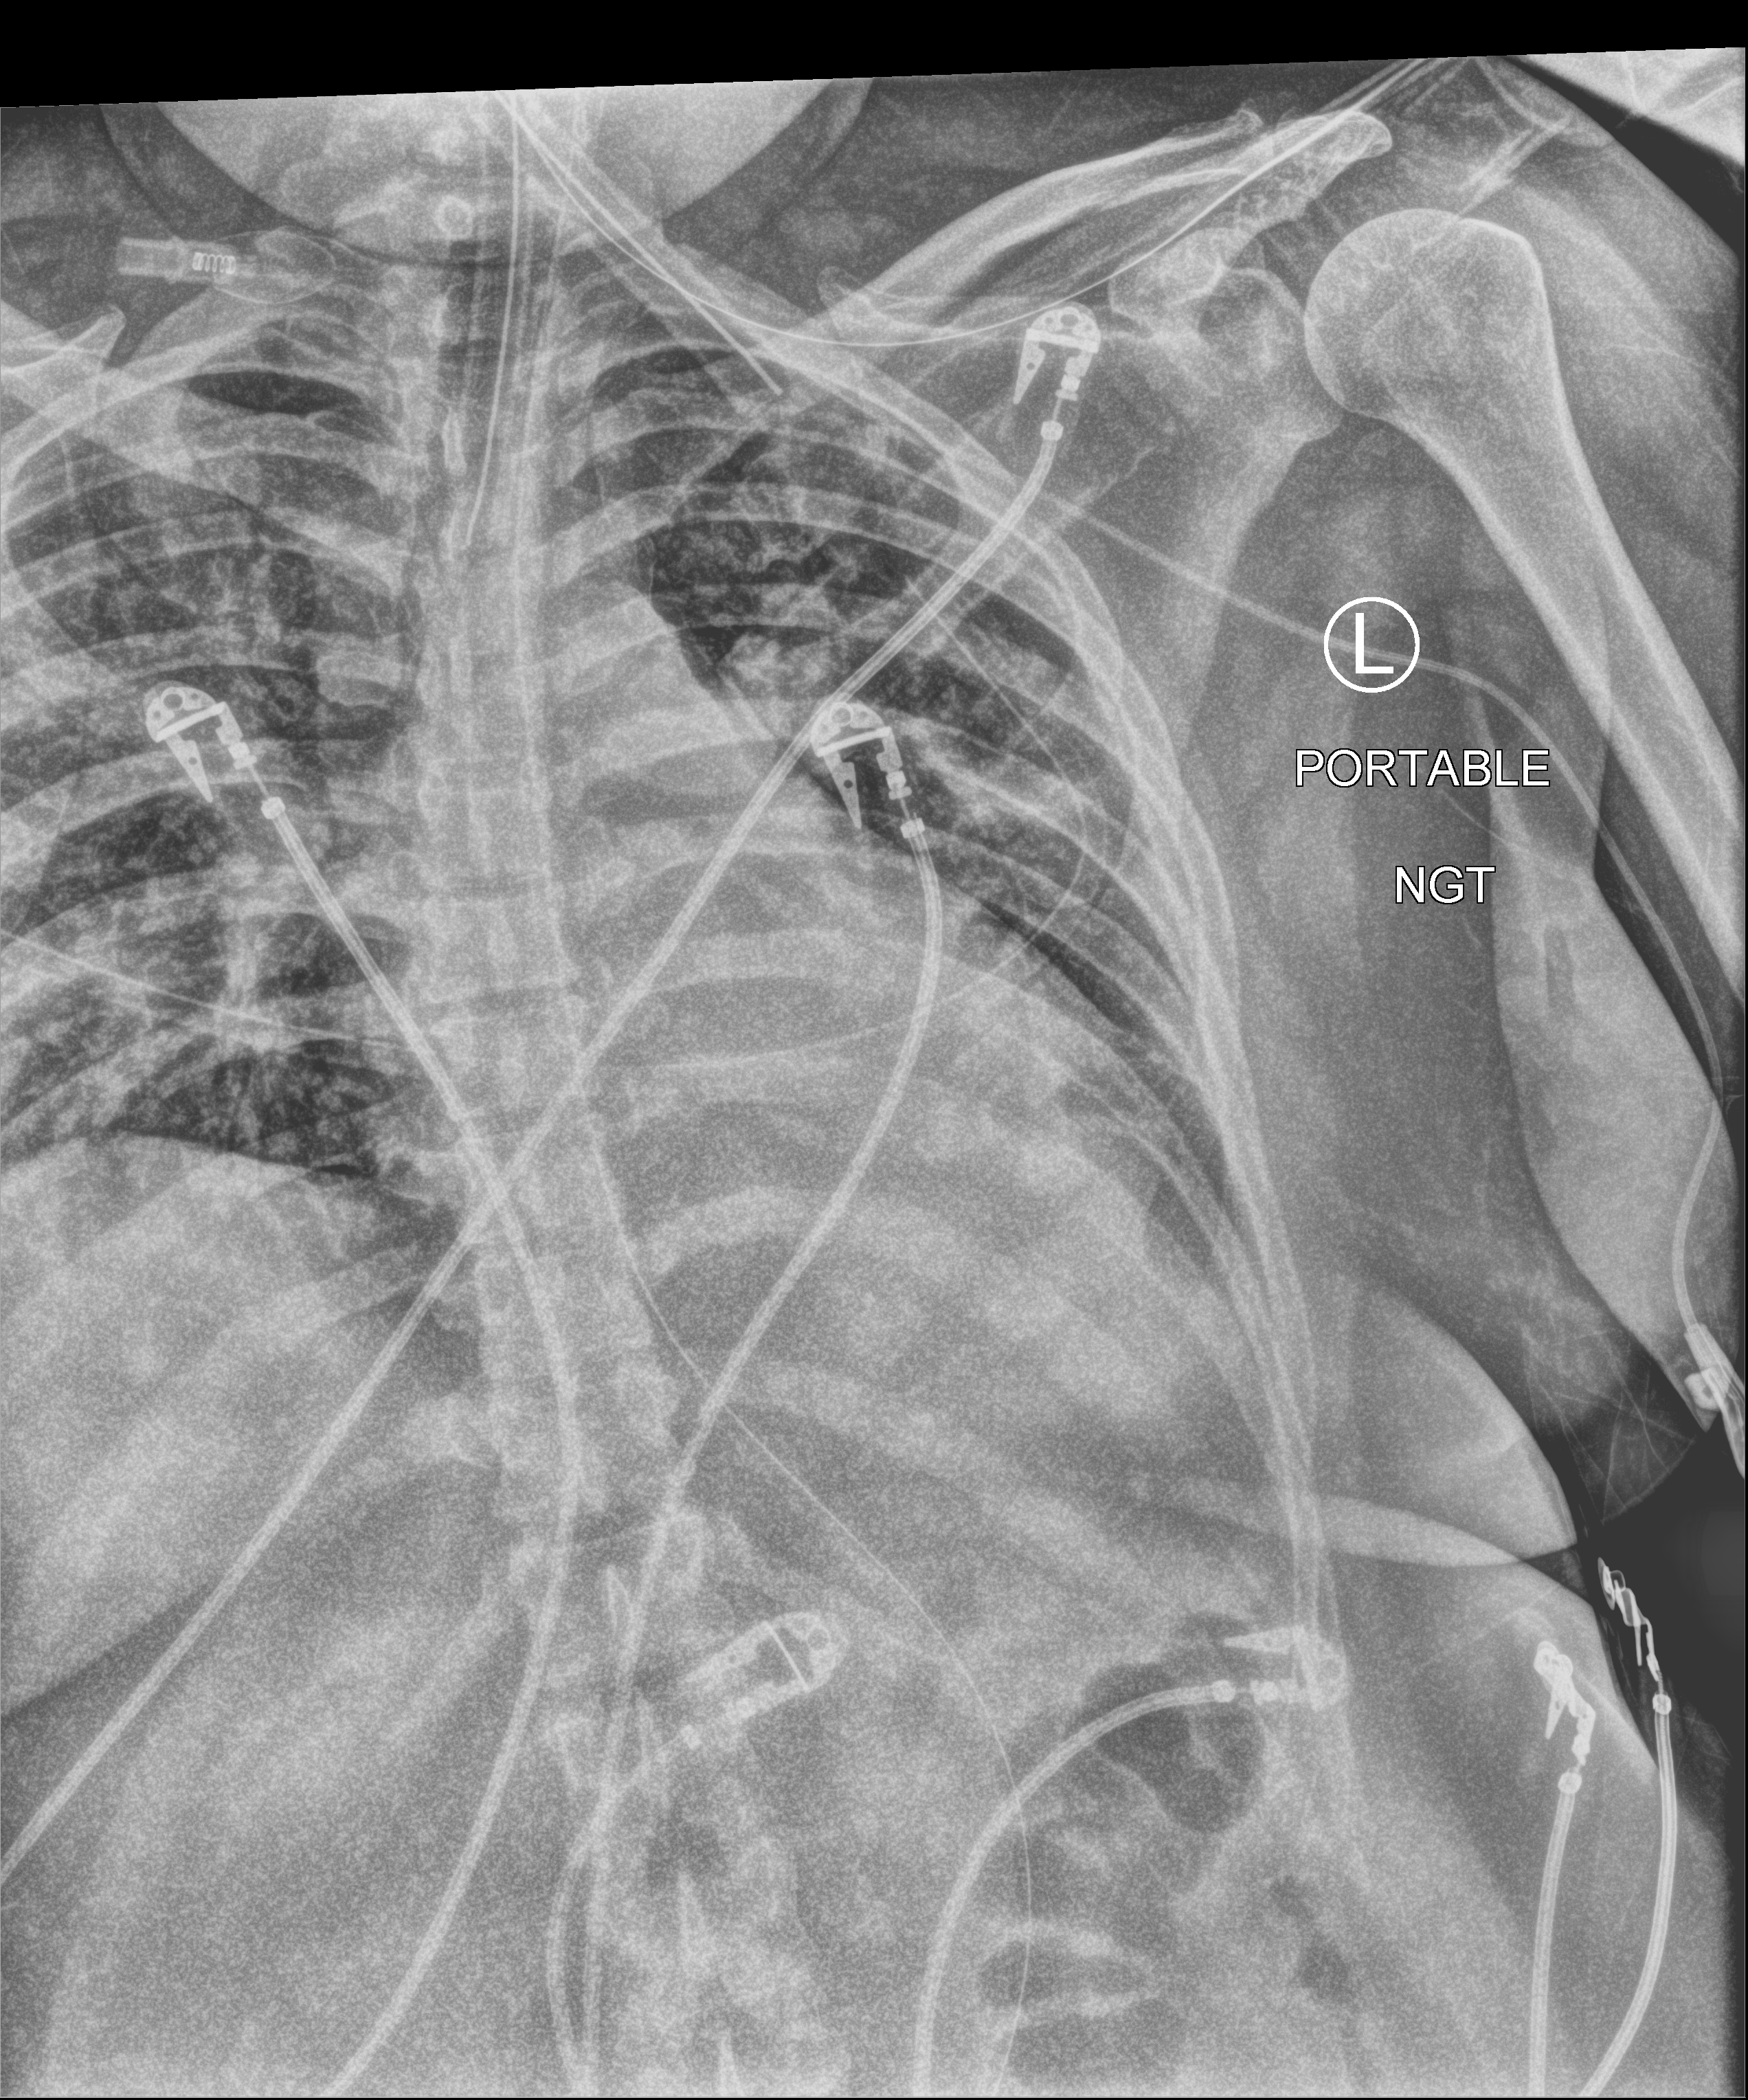
Chest X-ray (portable), anteroposterior (AP) projection. Patient hospitalised with COVID-19; female, aged 18–59 years.
From the hospital-stay record, not from the radiograph (when in the stay this image was taken is not recorded):
- diabetes (admission record): no